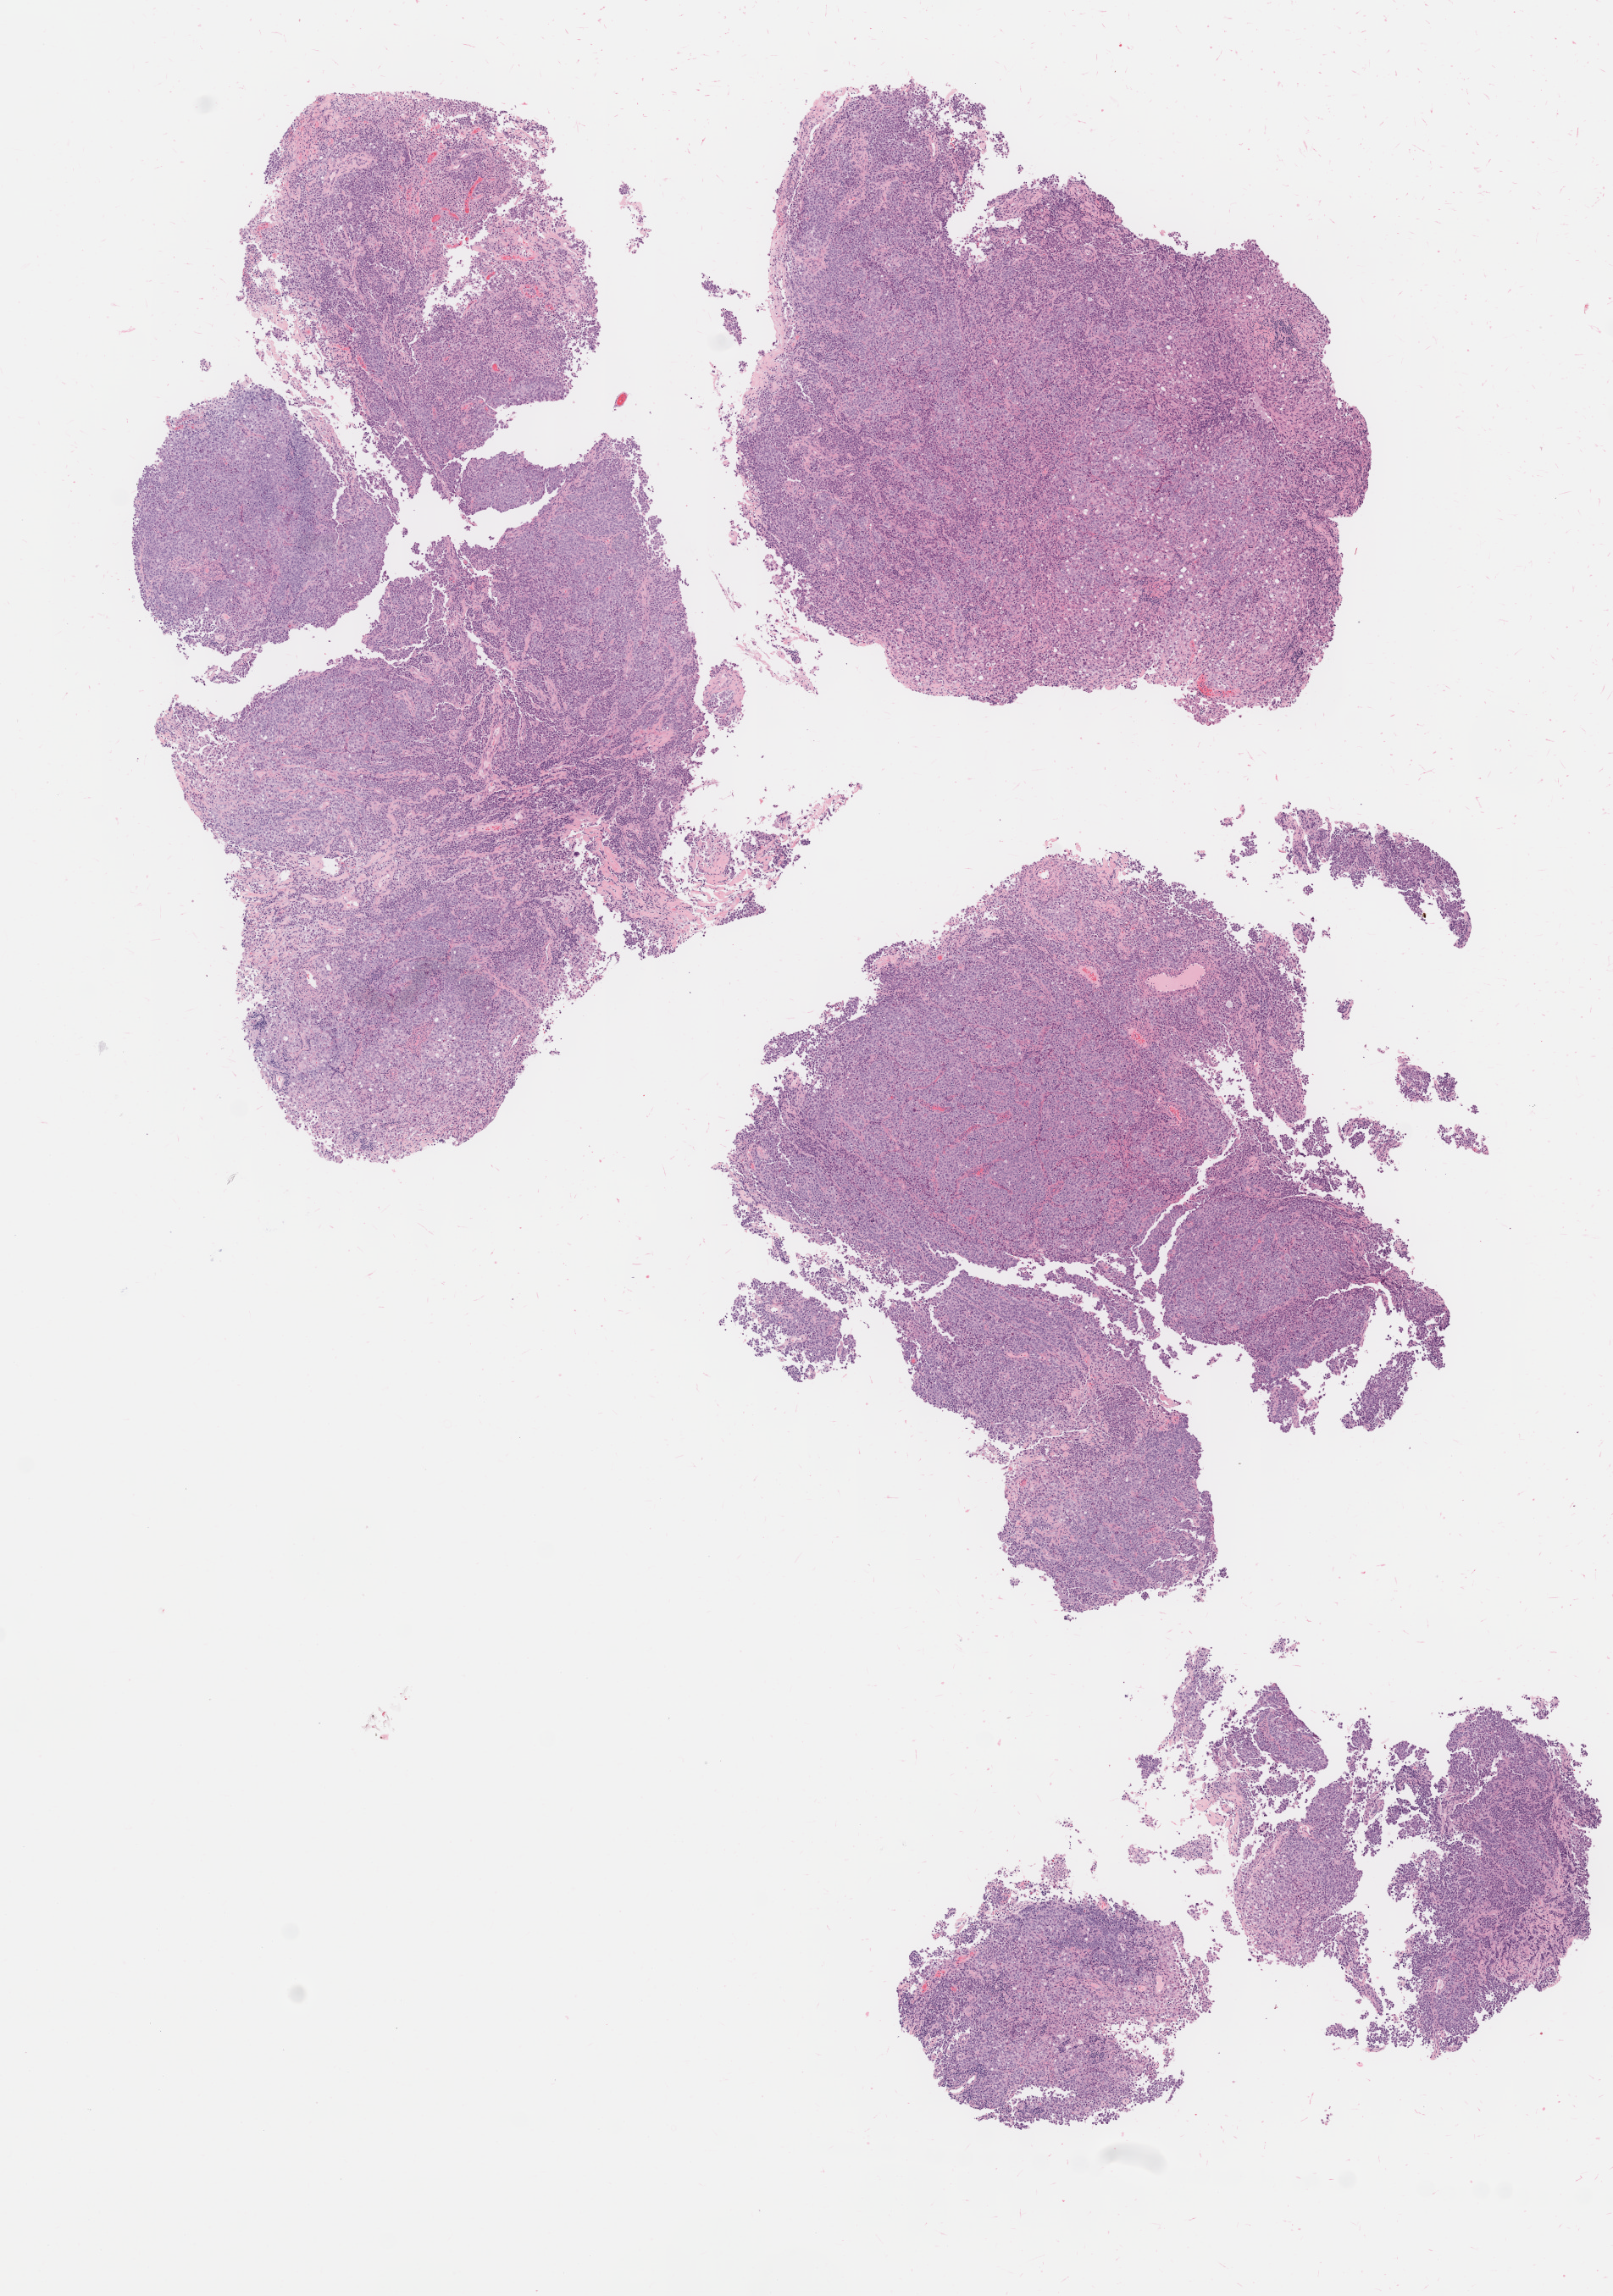
Digitized H&E-stained section, a low-resolution overview of the entire scanned area, about 7.6 x 10.8 mm; specimen: tumor tissue; anatomic site: cervix. Patient: female, 75 years old.
* diagnosis: Adenocarcinoma, NOS